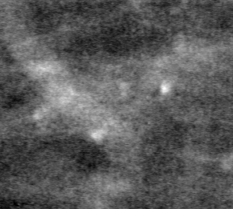
Crop from a digitized film mammogram around one marked abnormality, left breast, MLO view, BI-RADS breast density category 2 (scale 1–4).
Calcifications, morphology pleomorphic, distribution clustered; BI-RADS assessment category 4; pathology result (as recorded, not read from the image): benign.